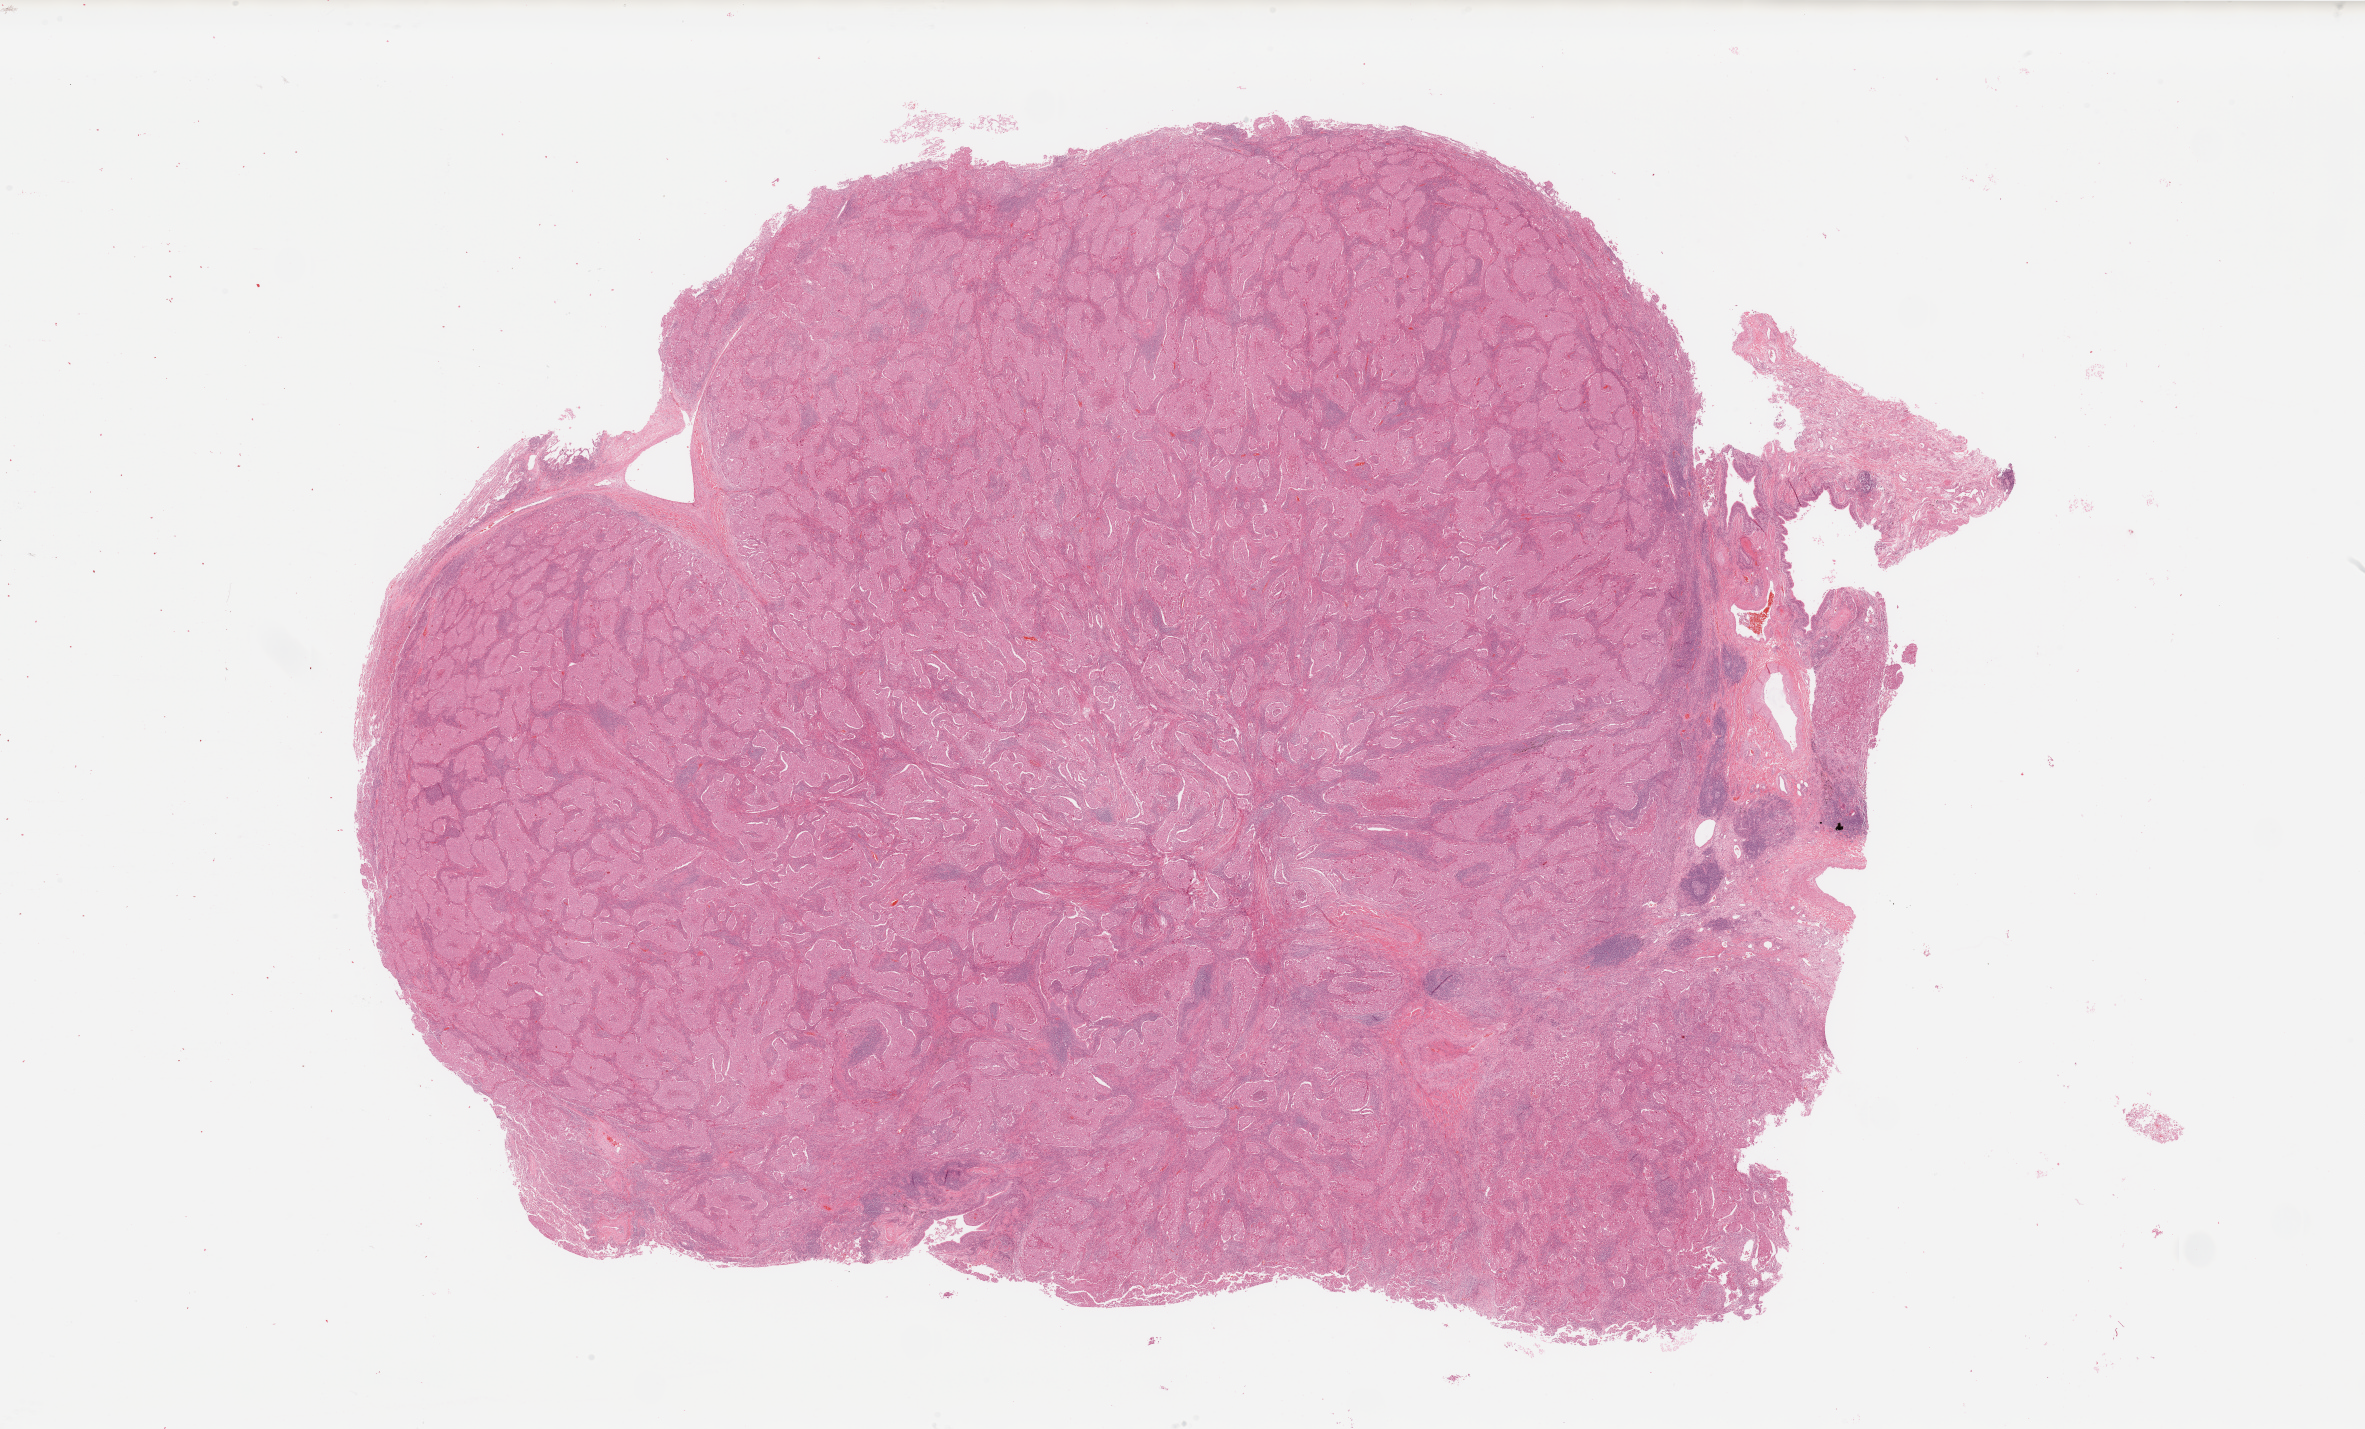
H&E whole-slide image, low-resolution overview of the scanned area, about 37.4 x 22.6 mm (from a 20x scan). Tumour tissue sample, sampled site: lung. Female, 48 y/o. Histologic grade: G3 (poorly differentiated). Slide review estimates, as recorded: tumour nuclei 75%, necrosis 5%.
Histologic diagnosis: Adenocarcinoma, NOS. AJCC pathologic stage: IIA.